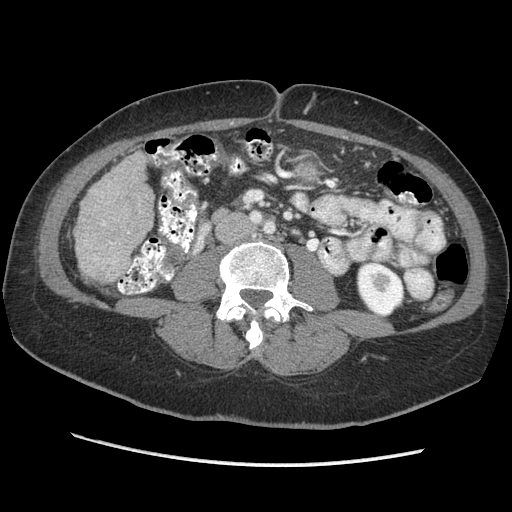
Contrast-enhanced abdominal CT (liver protocol), one axial slice; position 91 of 170 along the scan axis; soft-tissue window (W 400 / L 40 HU); 512 × 512 image matrix, field of view 360 × 360 mm. Case-level facts recorded for this patient, not image findings: diagnosis: hepatocellular carcinoma (patient treated with transarterial chemoembolisation; whether this scan precedes or follows treatment is not stated here); TNM stage (as recorded): Stage-II; Child-Pugh class: A; tumour differentiation: no biopsy; tumour nodularity: multinodular.
Annotated regions visible in this slice (semi-automatically segmented with operator editing):
- liver parenchyma outside the tumour (the mass and vessels are separate outlines, so this box may not span the whole liver): bounding box <74,152,154,280> (left, top, right, bottom; pixels)
- liver vessels: <96,223,112,260>